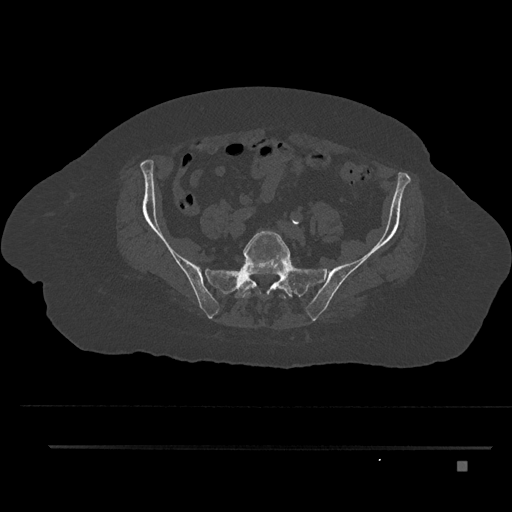
CT including the spine, one axial slice; position 17 of 797 along the scan axis; reconstruction kernel Br40s/3; bone window (W 1800 / L 400 HU); 0.5 mm slice thickness; 512 × 512 image matrix, field of view 437 × 437 mm. Patient: female, 76 years. From the clinical record (not read from this slice): primary cancer: lung; vertebrae with lytic lesions (as recorded): T11, L3.
Outlined on this slice (semi-automatically segmented with operator editing):
- L5 vertebra: box from (x=242, y=230) to (x=290, y=300) px